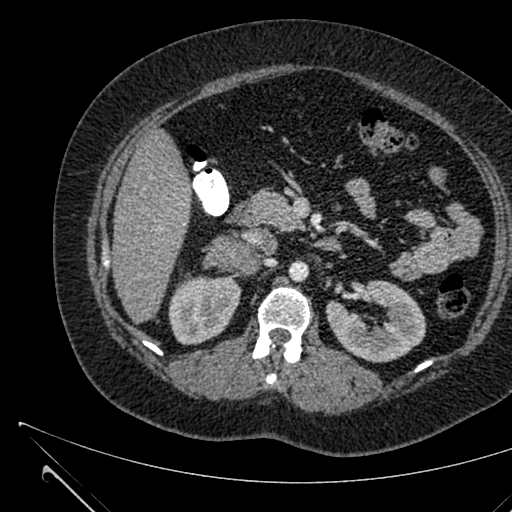
Contrast-enhanced abdominal CT, one axial slice. Position 356 of 731 along the scan axis. 120 kVp. Intravenous contrast given. Soft-tissue window (W 400 / L 40 HU). 1 mm slice thickness. 512 × 512 image matrix, field of view 376 × 376 mm. Patient: female, 36 years. Case-level facts recorded for this patient, not image findings: diagnosis: adrenocortical carcinoma; tumour side: right adrenal; tumour size at pathology: 10 cm; Ki-67 index: 20 %; stage (as recorded): 4.
Outlined on this slice (semi-automatically segmented with operator editing):
- mass: box from (x=208, y=236) to (x=253, y=271) px